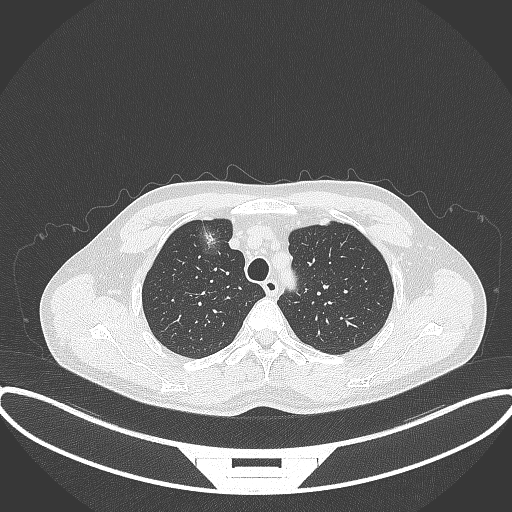
Chest CT, one axial slice. Slice 292 of 395 in the series (ordered by position). Reconstruction kernel B70f. 120 kVp. Lung window (W 1500 / L -600 HU). 1 mm slice thickness. 512 × 512 image matrix. Patient: male, 60 years. From the clinical record (not read from this slice): clinical TNM (as recorded): T1c N0 M0.
Annotated regions visible in this slice (bounding box drawn by a radiologist):
- lung tumour (recorded histology: adenocarcinoma): box from (x=191, y=216) to (x=223, y=259) px